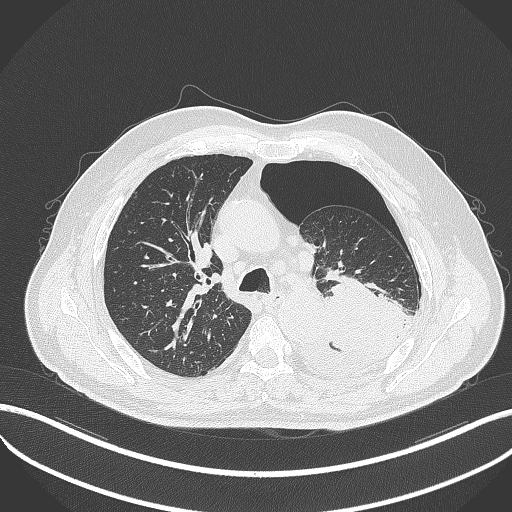
Chest CT, one axial slice. Position 349 of 464 along the scan axis. Reconstruction kernel B70f. 120 kVp. Lung window (W 1500 / L -600 HU). 1 mm slice thickness. 512 × 512 image matrix. Male patient, age 76 years. From the clinical record (not read from this slice): clinical TNM (as recorded): T3 N0 M1b.
Structures marked on this image (bounding box drawn by a radiologist):
- lung tumour (recorded histology: adenocarcinoma): bounding box <326,271,405,353> (left, top, right, bottom; pixels)